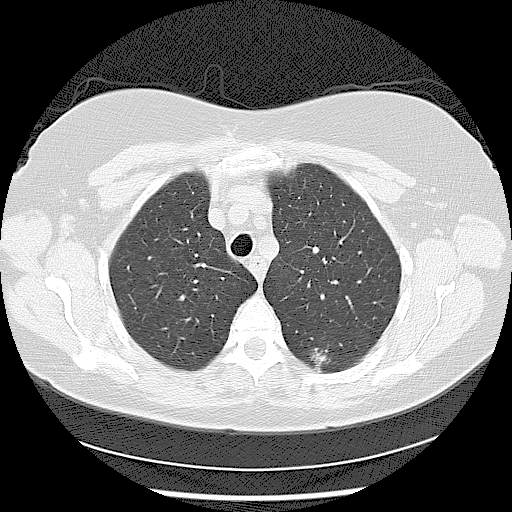
Axial slice from a low-dose chest CT screening exam. Baseline annual screen. Lung window (W 1500 / L -600 HU). Lung (sharp) reconstruction kernel (LUNG). Slice 25 of 116 in the series. 512 × 512 image matrix, field of view 360 × 360 mm. Female, age 56 years at enrolment. Current smoker at enrolment.
Expert reader's lesion annotation, bounding box (x1, y1, x2, y2) in pixels: (295, 333, 345, 382). The screening reader recorded 2 non-calcified nodules or masses ≥4 mm on this exam (left lower lobe, left lower lobe); which of them this box marks is not recorded. Official screen result: positive, change unspecified: nodule(s) >= 4 mm or enlarging nodule(s), mass(es), or other non-specific abnormalities suspicious for lung cancer. Later outcome: lung cancer diagnosed 638 days after this screen (after the second annual screen) — adenocarcinoma, NOS, left lower lobe, moderately differentiated (G2), stage IIA (AJCC 6th edition), 15 mm at pathology.